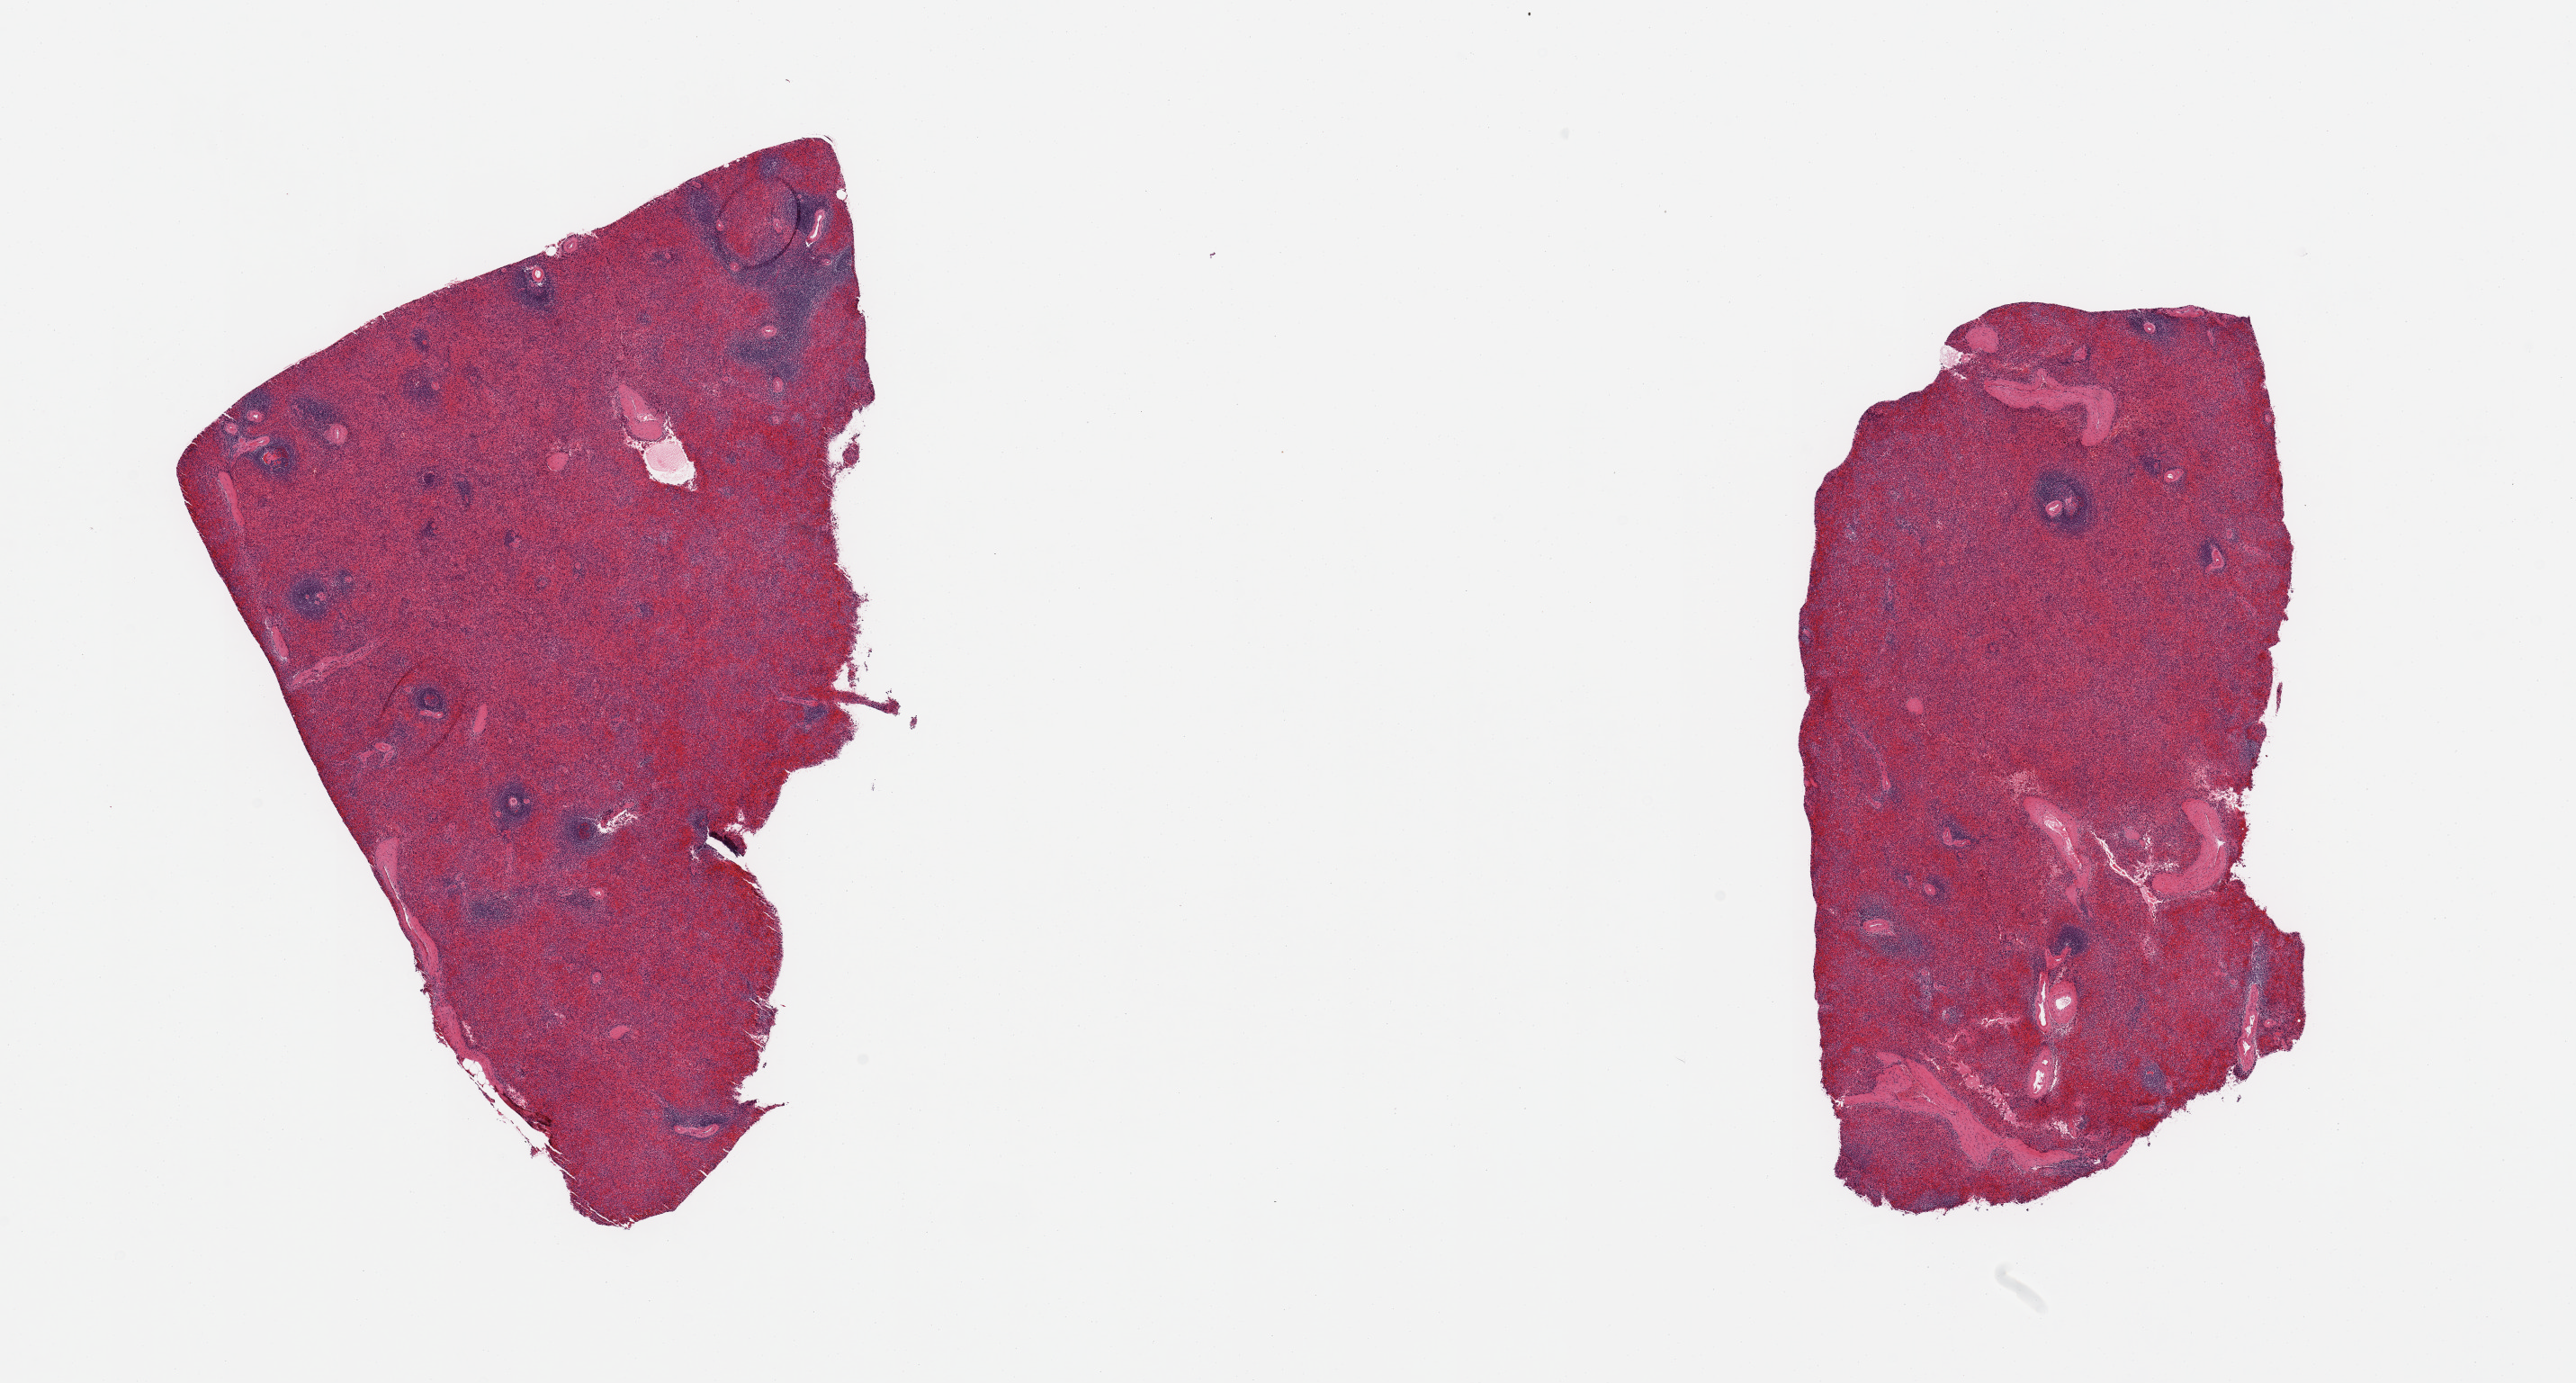
H&E whole-slide image, whole scanned area (about 22.6 x 12.2 mm) shown as a low-resolution overview. PAXgene-fixed, paraffin-embedded tissue. Section of spleen (target tissue). Tissue donor sample. Donor sex: female.
- reviewer comment on this tissue sample: 2 pieces; mild congestion